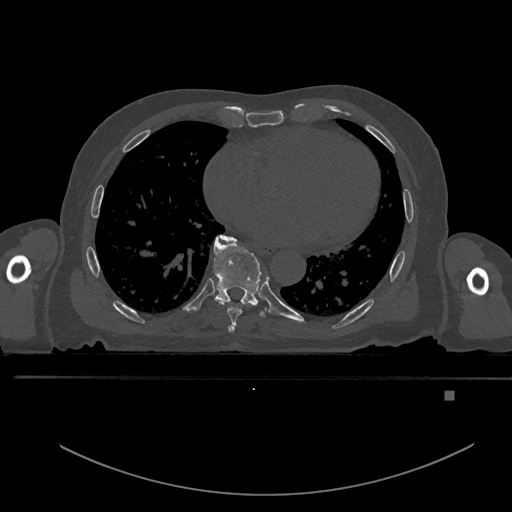
CT including the spine, one axial slice; slice 225 of 969 in the series (ordered by position); bone window (W 1800 / L 400 HU); 0.5 mm slice thickness; 512 × 512 image matrix, field of view 456 × 456 mm. Male patient, age 82 years. Case-level facts recorded for this patient, not image findings: primary cancer: prostate; vertebrae with lytic lesions (as recorded): T11, T9, T8, T2.
Annotated regions visible in this slice (semi-automatic segmentation, software-assisted and operator-edited):
- T6 vertebra: bounding box [x1, y1, x2, y2] px = [228, 326, 234, 333]
- T7 vertebra: [219, 235, 267, 325]
- T8 vertebra: [213, 236, 265, 317]